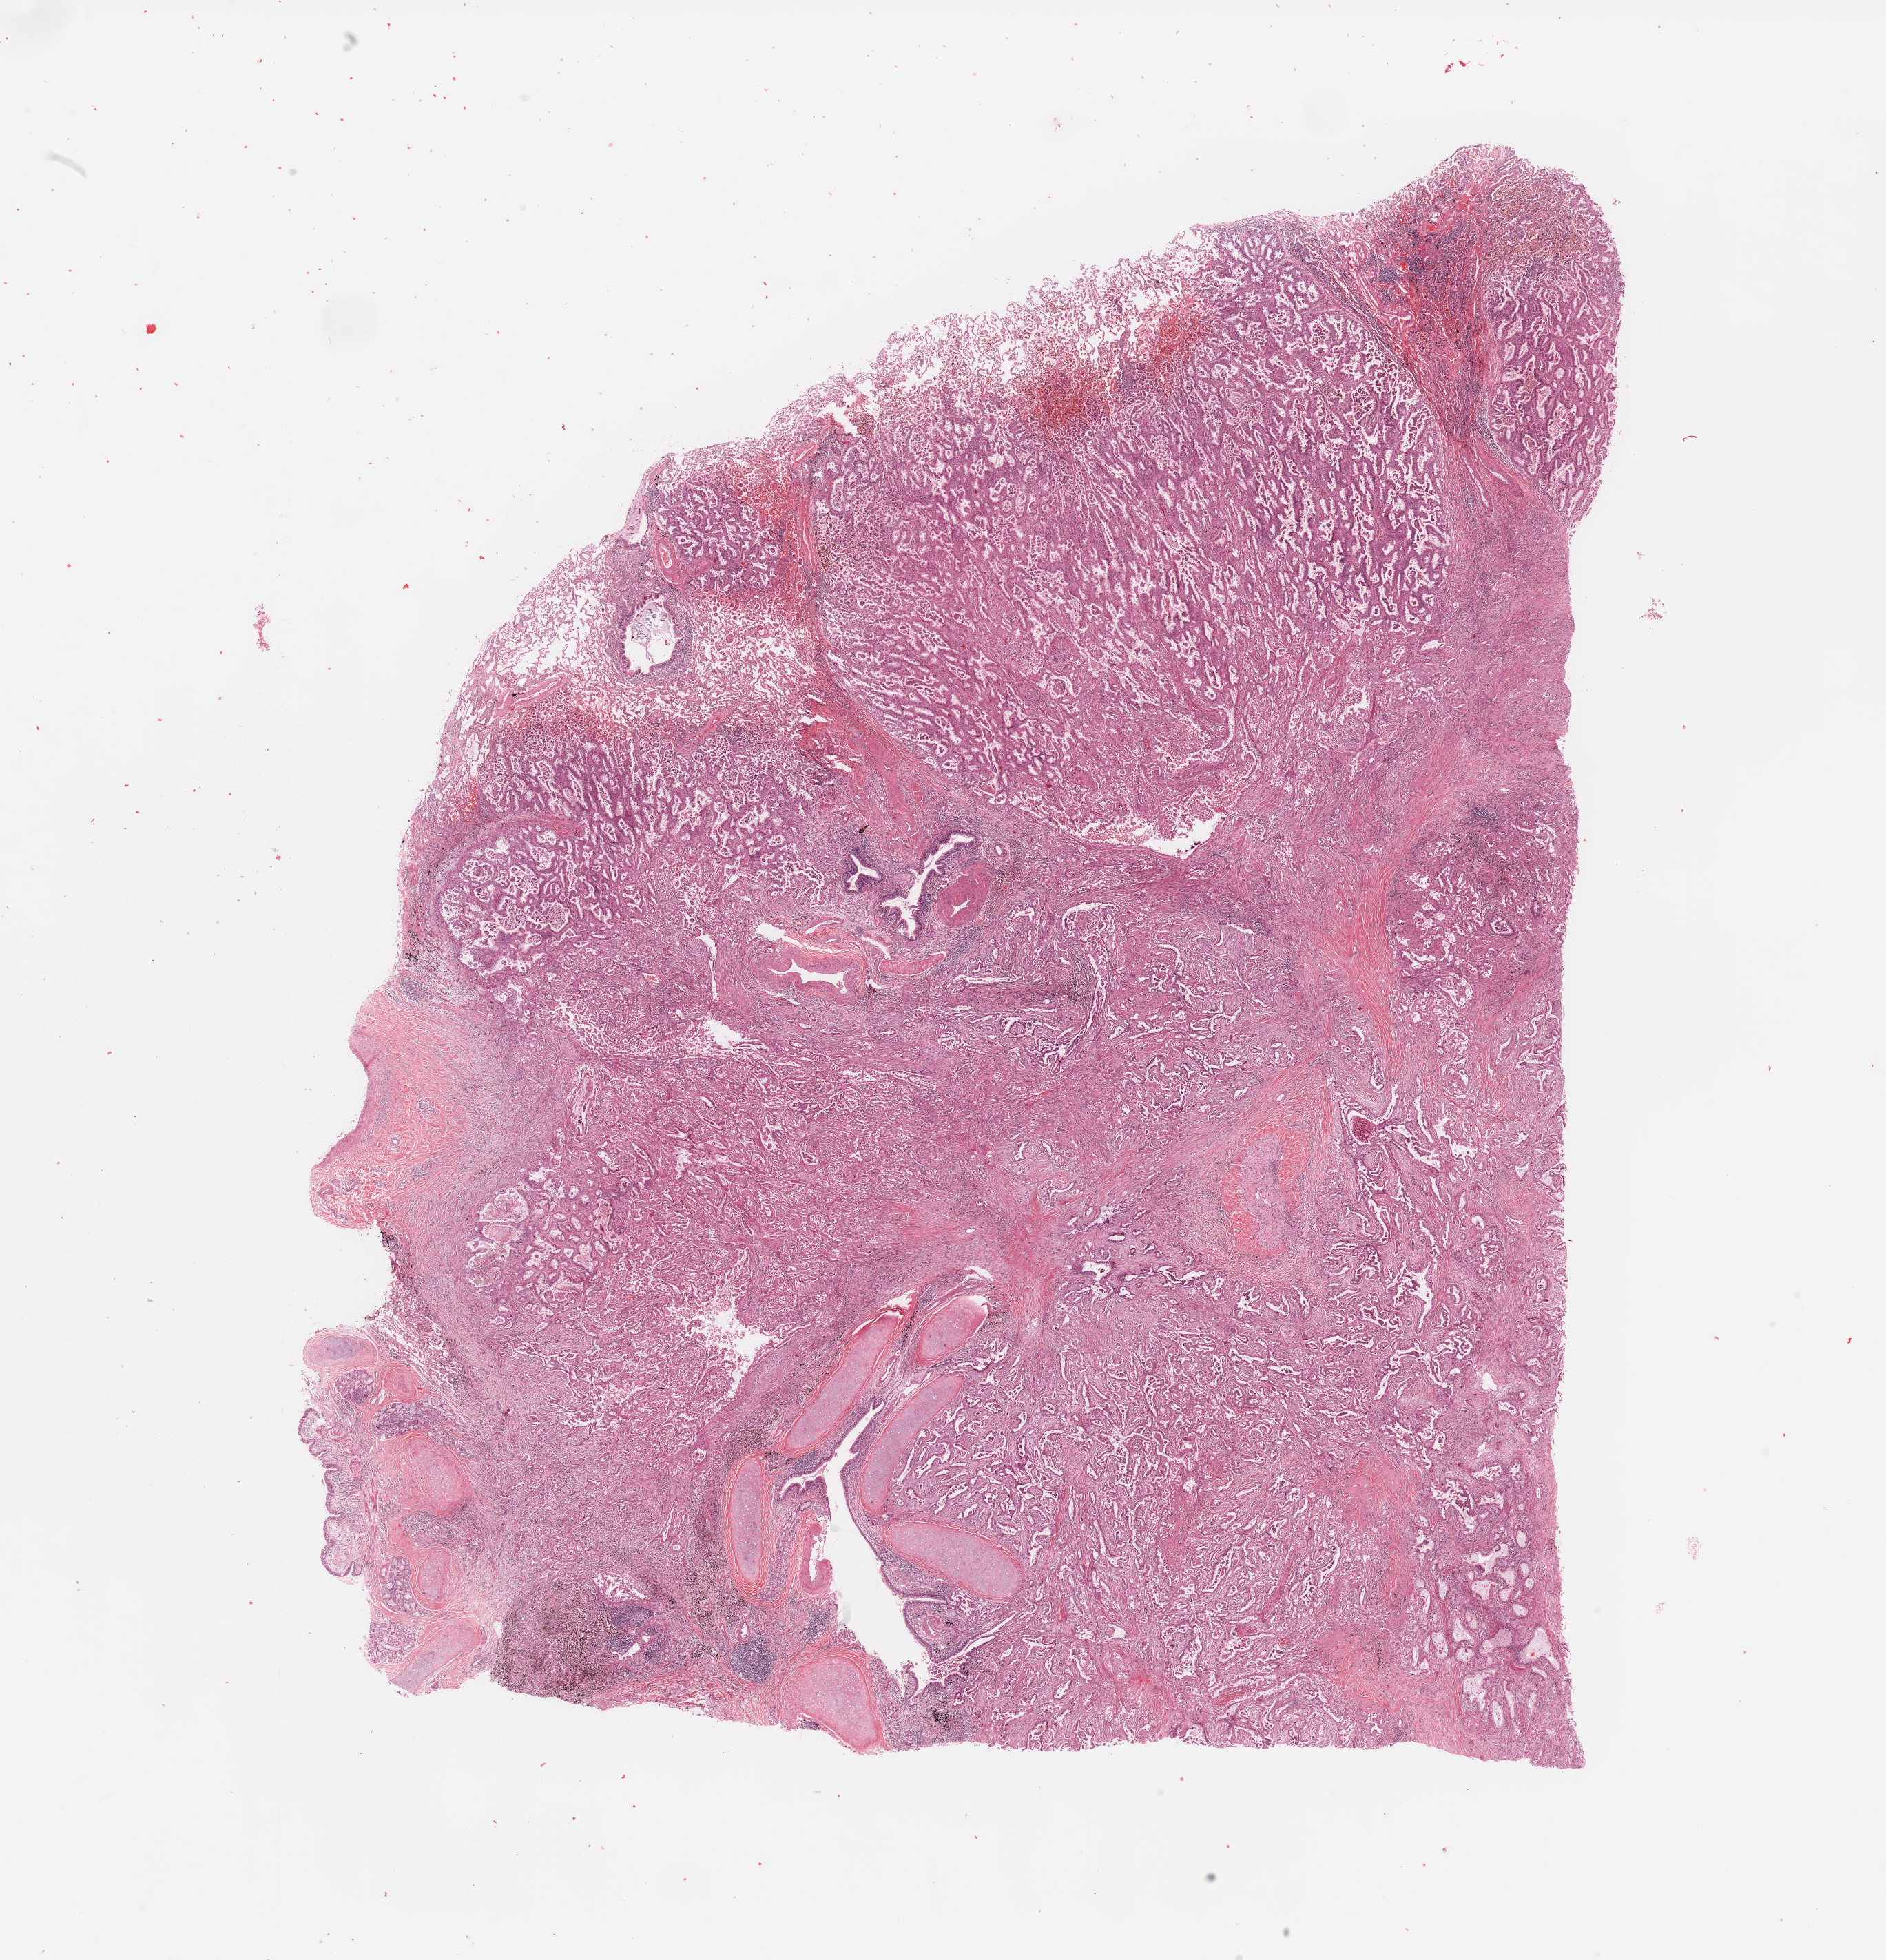
Whole-slide histology image, H&E — a low-resolution overview of the entire scanned area, about 21.7 x 22.5 mm (from a 20x scan), lung, tumour tissue. Male, 60 y/o. Histologic grade: G2 (moderately differentiated).
Histologic diagnosis: Adenocarcinoma, NOS. AJCC pathologic stage: IIB.